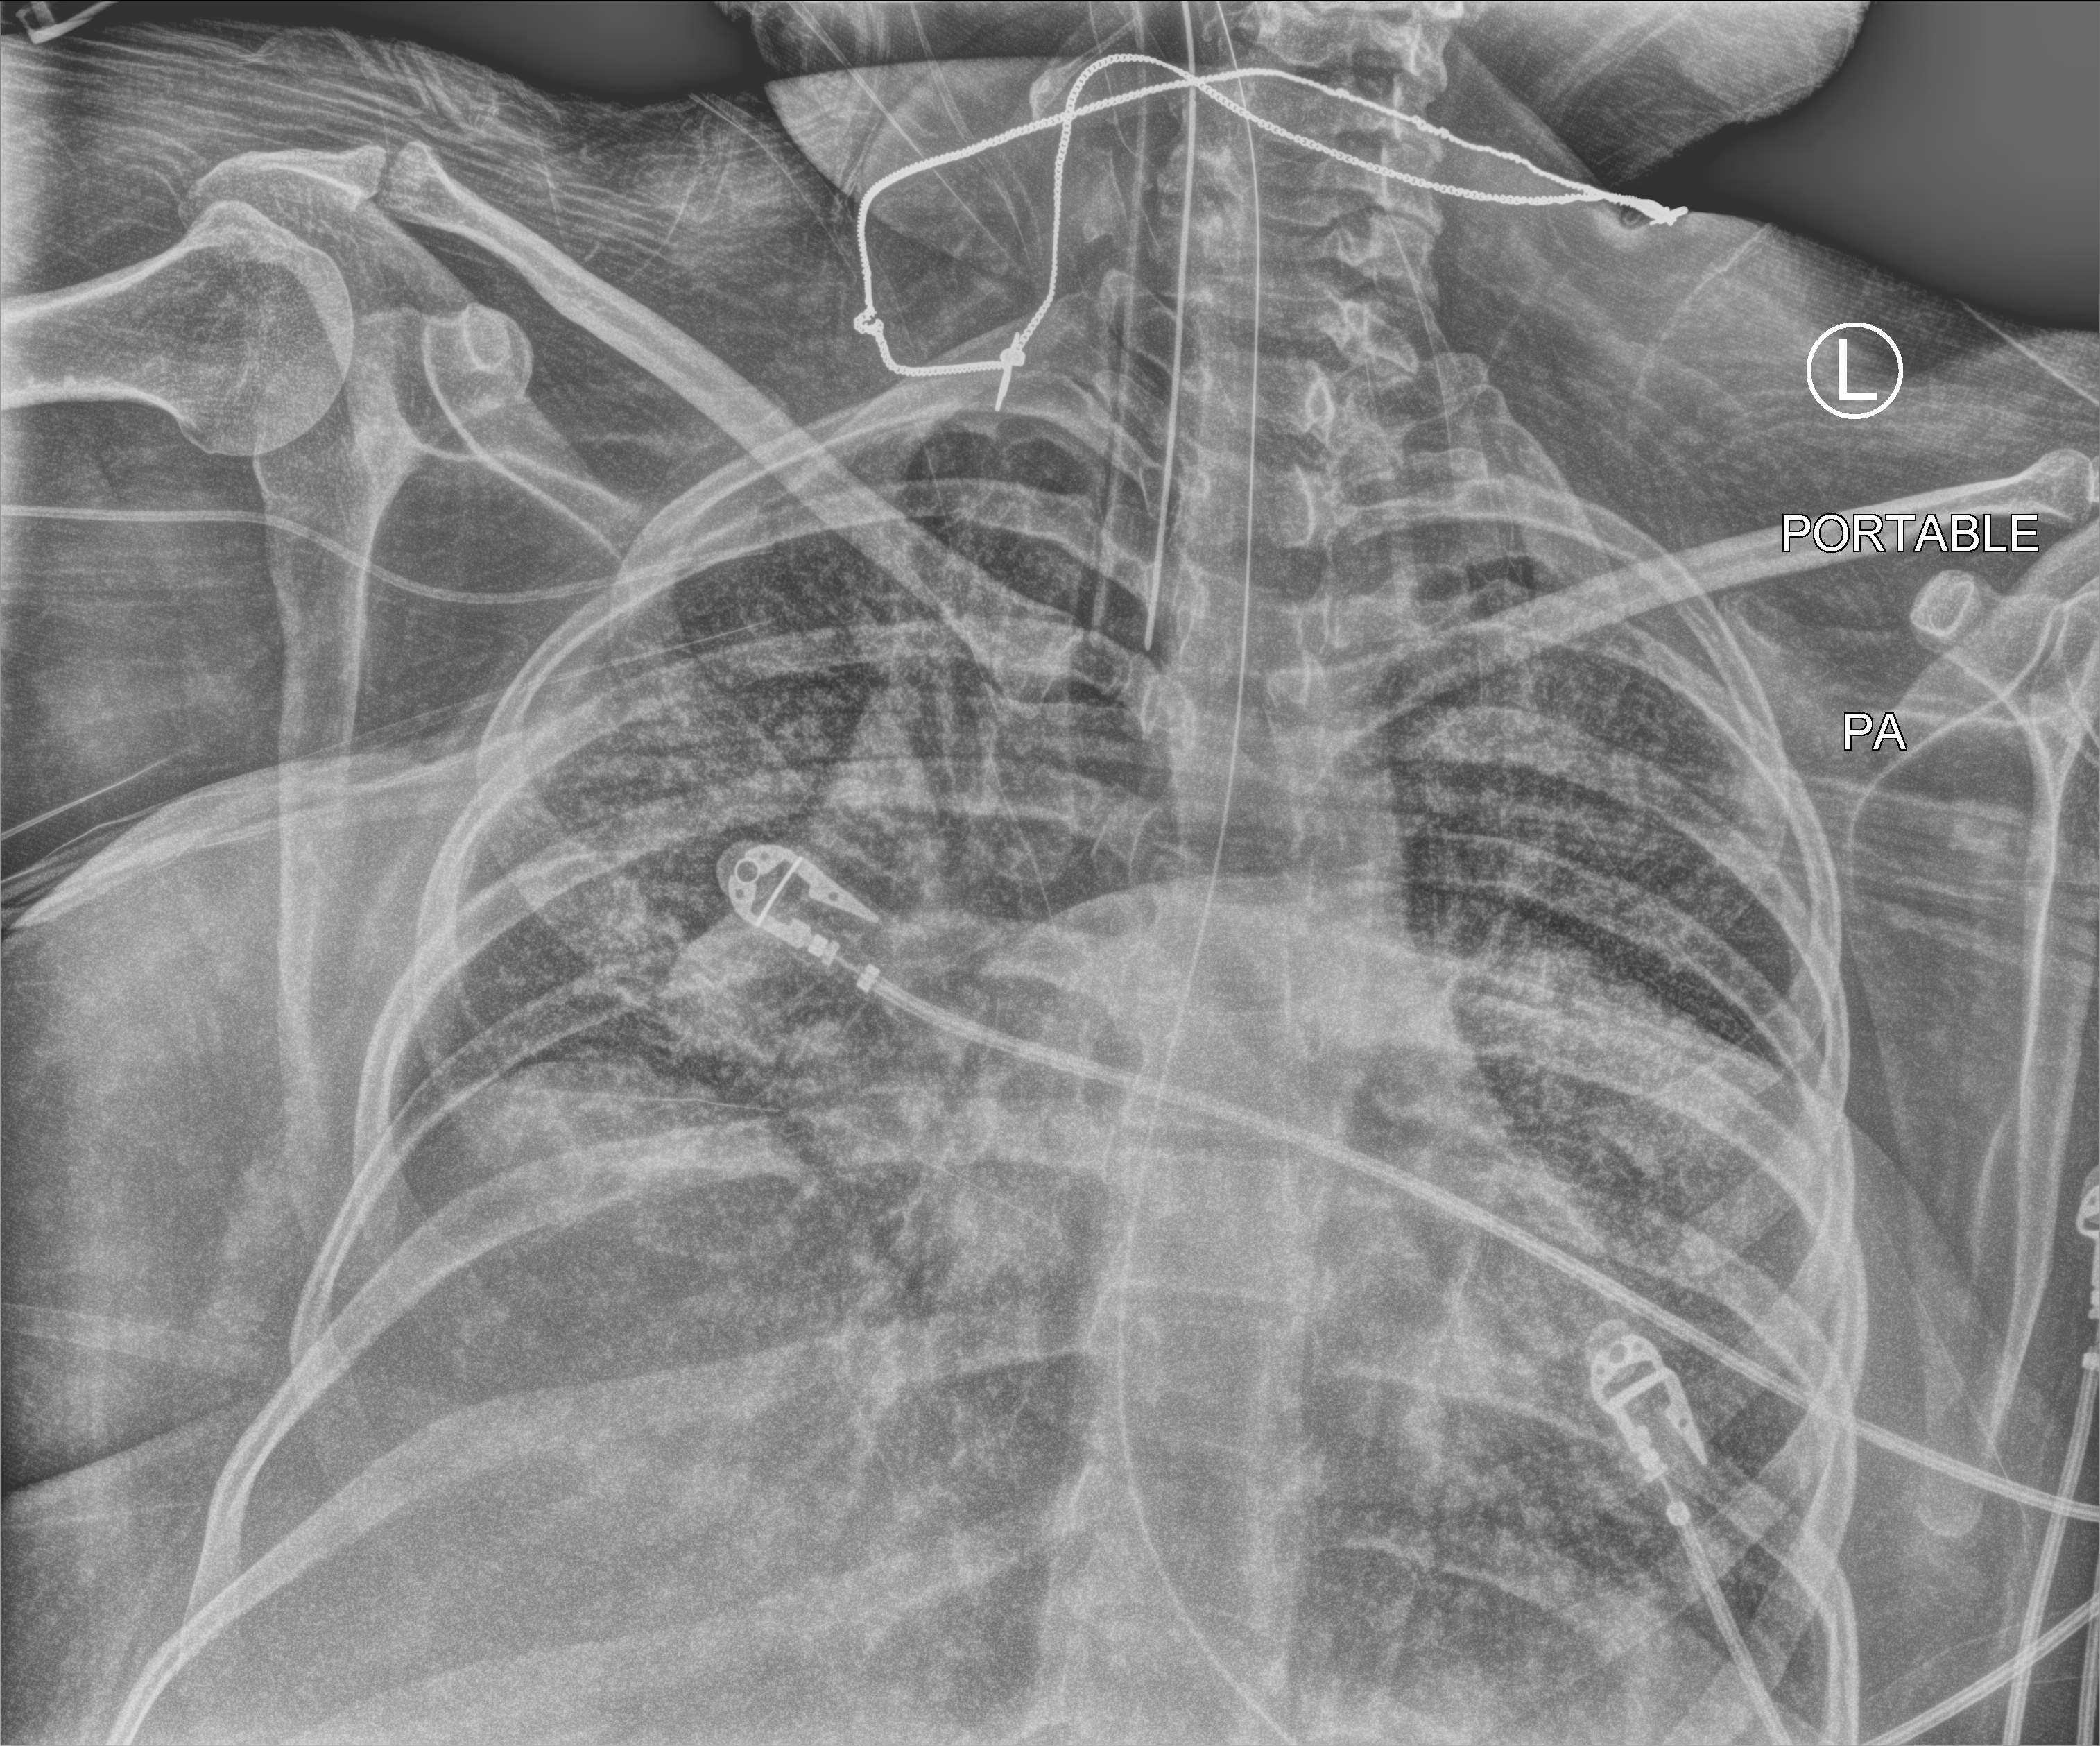
Bedside chest radiograph (computed radiography); anteroposterior (AP) projection. Patient hospitalised with COVID-19; female, aged 18–59 years.
Hospital-stay facts (about this admission, not read from this image; timing relative to this image not recorded): admitted to intensive care during this hospital stay: yes; mechanically ventilated during this hospital stay: yes.